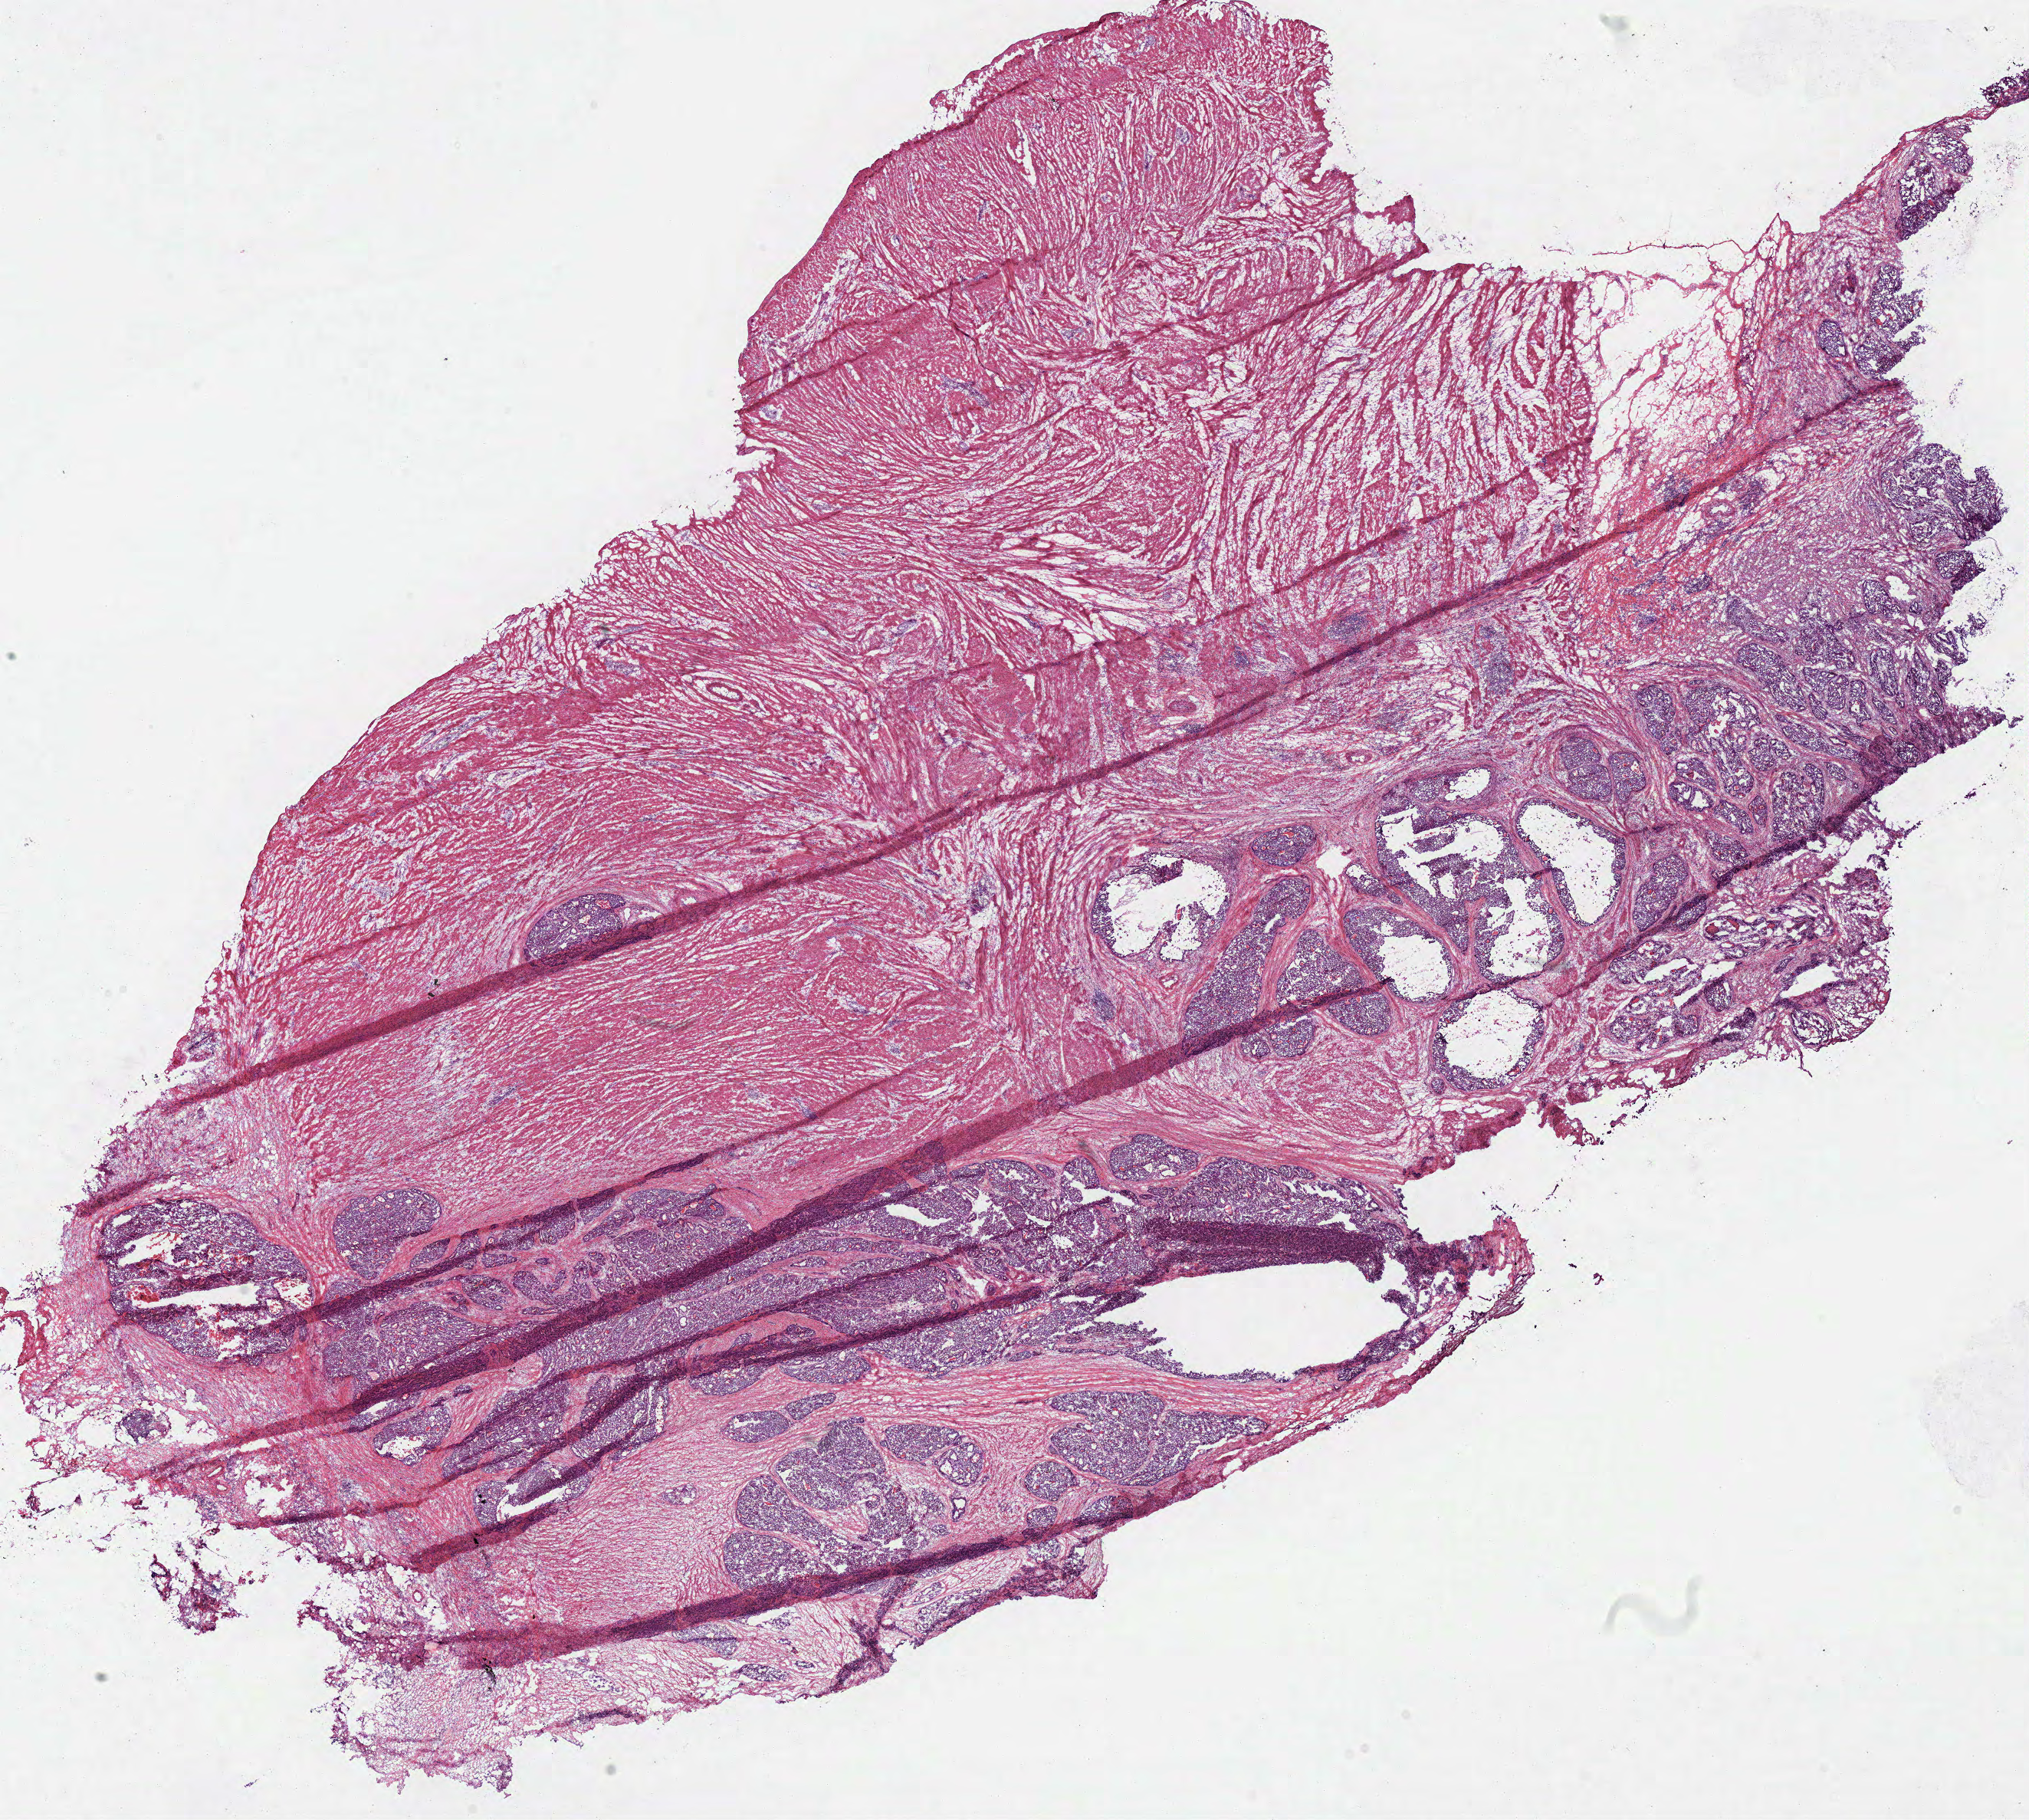
Hematoxylin and eosin (H&E) stained whole-slide image, whole scanned area (about 20.9 x 18.7 mm) shown as a low-resolution overview; frozen section; sample: primary tumour, stomach. Patient: male, age at initial diagnosis 69 years. Histologic grade: GX (grade cannot be assessed). Pathologist review of this section (percent, as recorded): tumour cells 45%, tumour nuclei 70%, normal cells 57%, stromal cells 0%, necrosis 3%. Inflammatory infiltration, as recorded: lymphocyte infiltration 10%, monocyte infiltration 0%, neutrophil infiltration 0%.
Diagnosis: Adenocarcinoma, NOS (gastric antrum). Lymph nodes positive (case pathology): 0 of 15 examined. AJCC pathologic stage: II (7th edition).